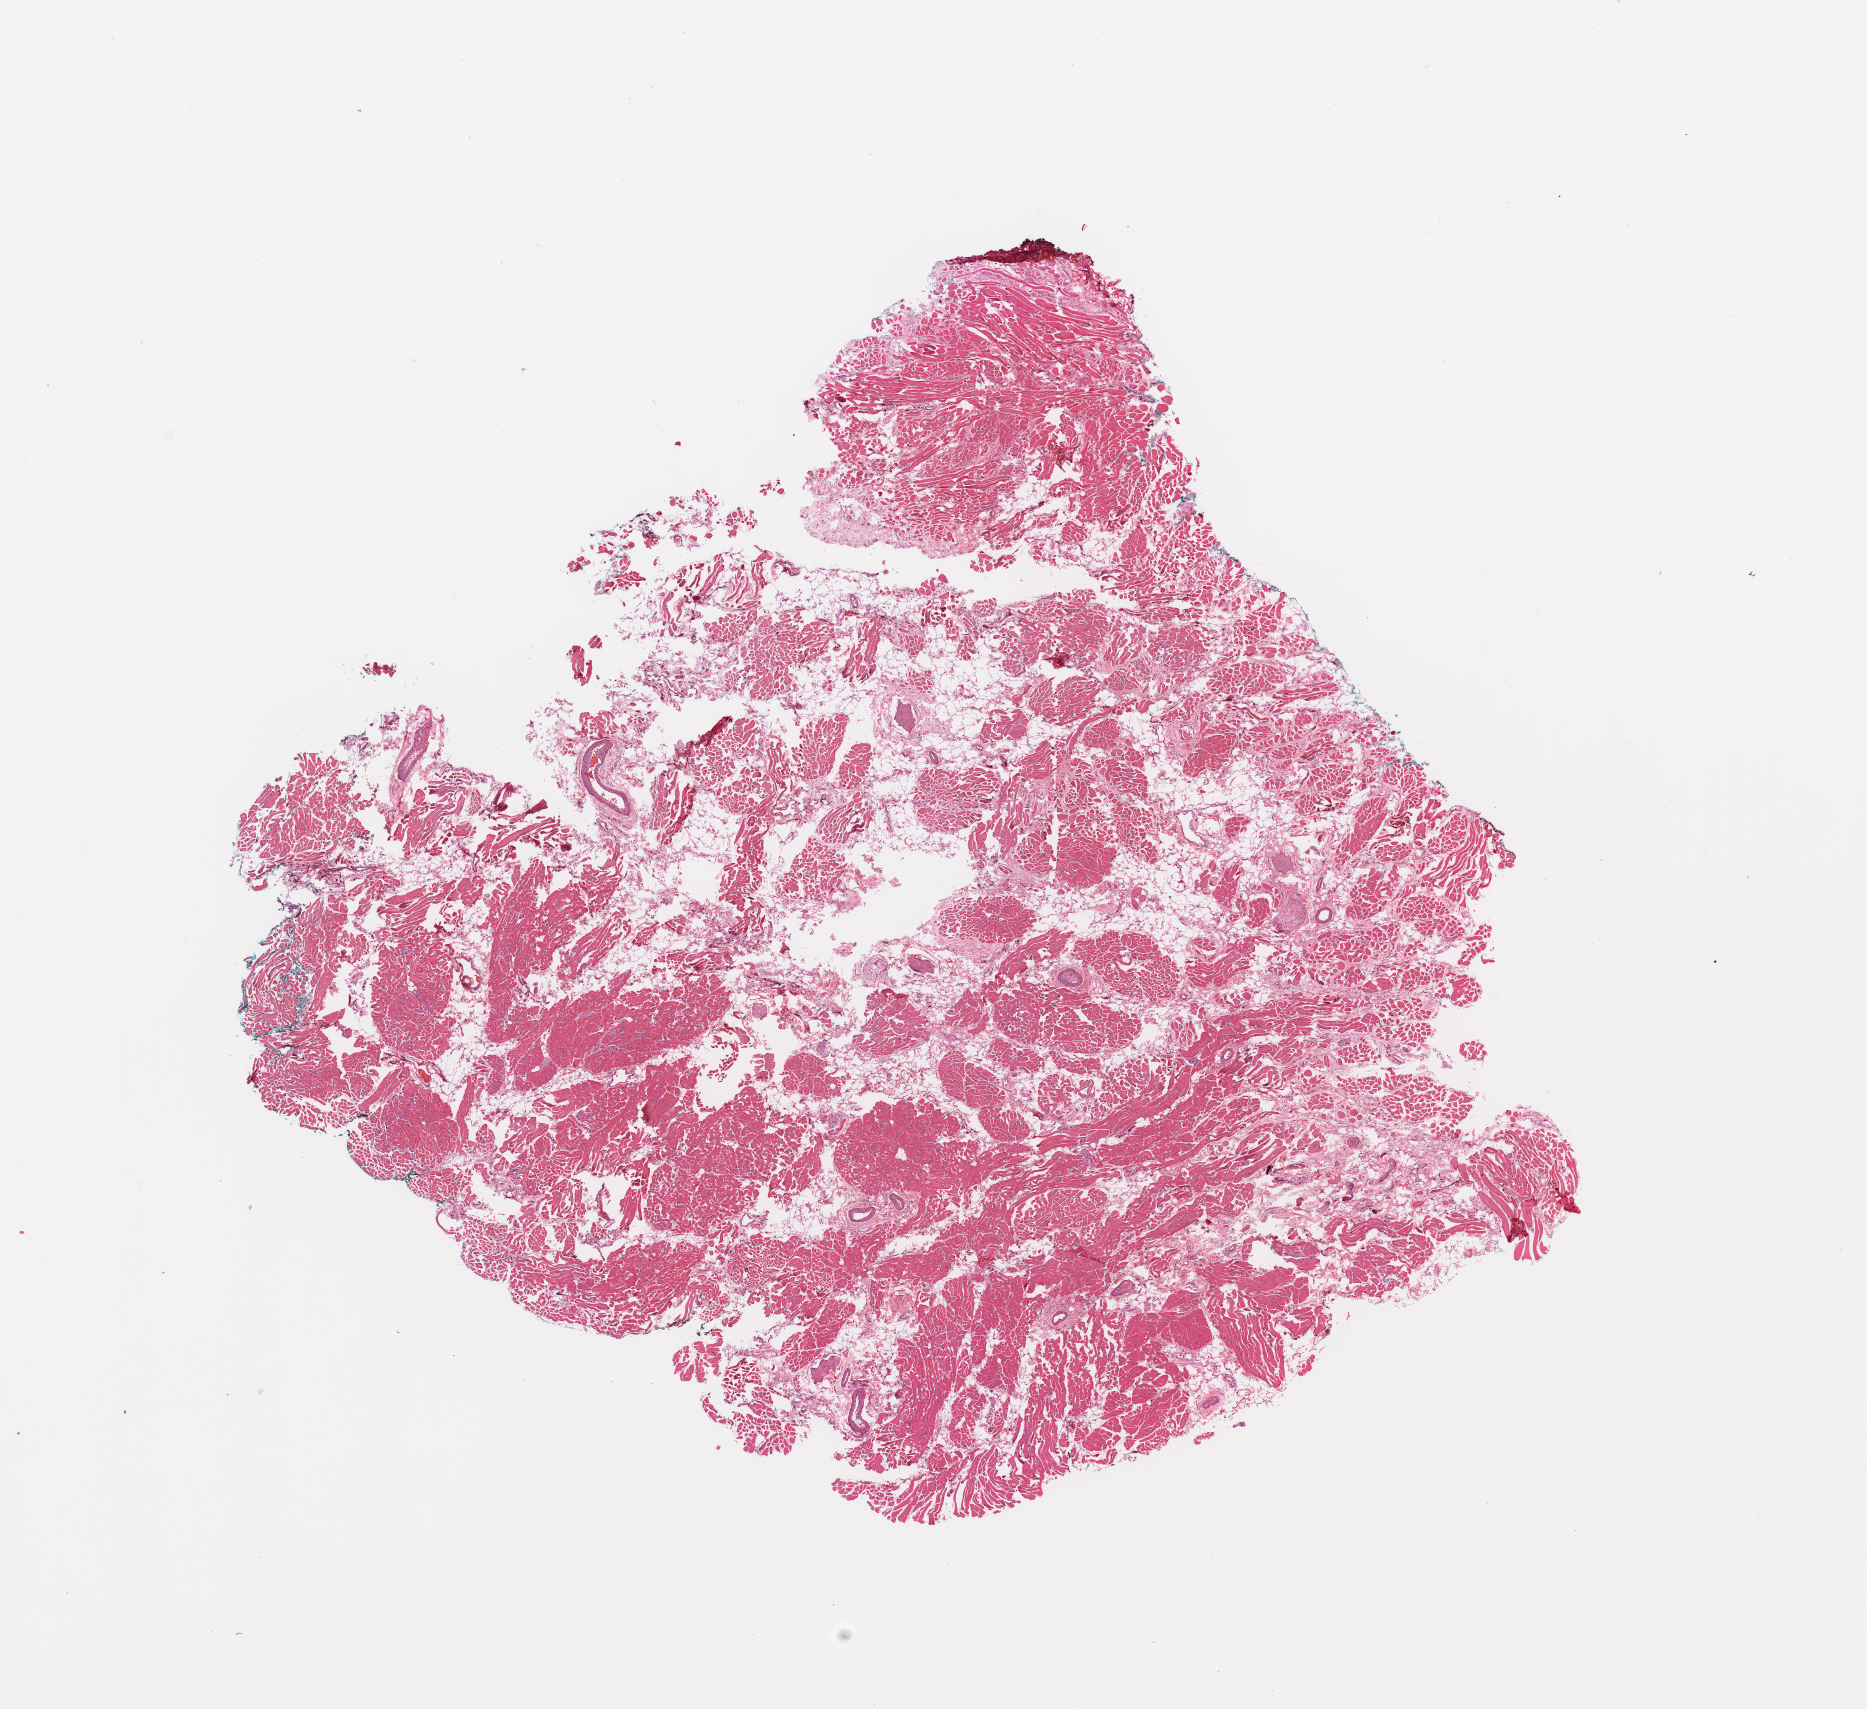
Digitized Hematoxylin and eosin (H&E) stained tissue section (whole slide), low-resolution overview of the scanned area, about 14.8 x 13.5 mm. Head and neck, tissue type not recorded. 61-year-old male patient.
• patient diagnosis: Squamous cell carcinoma, NOS (tongue, NOS)